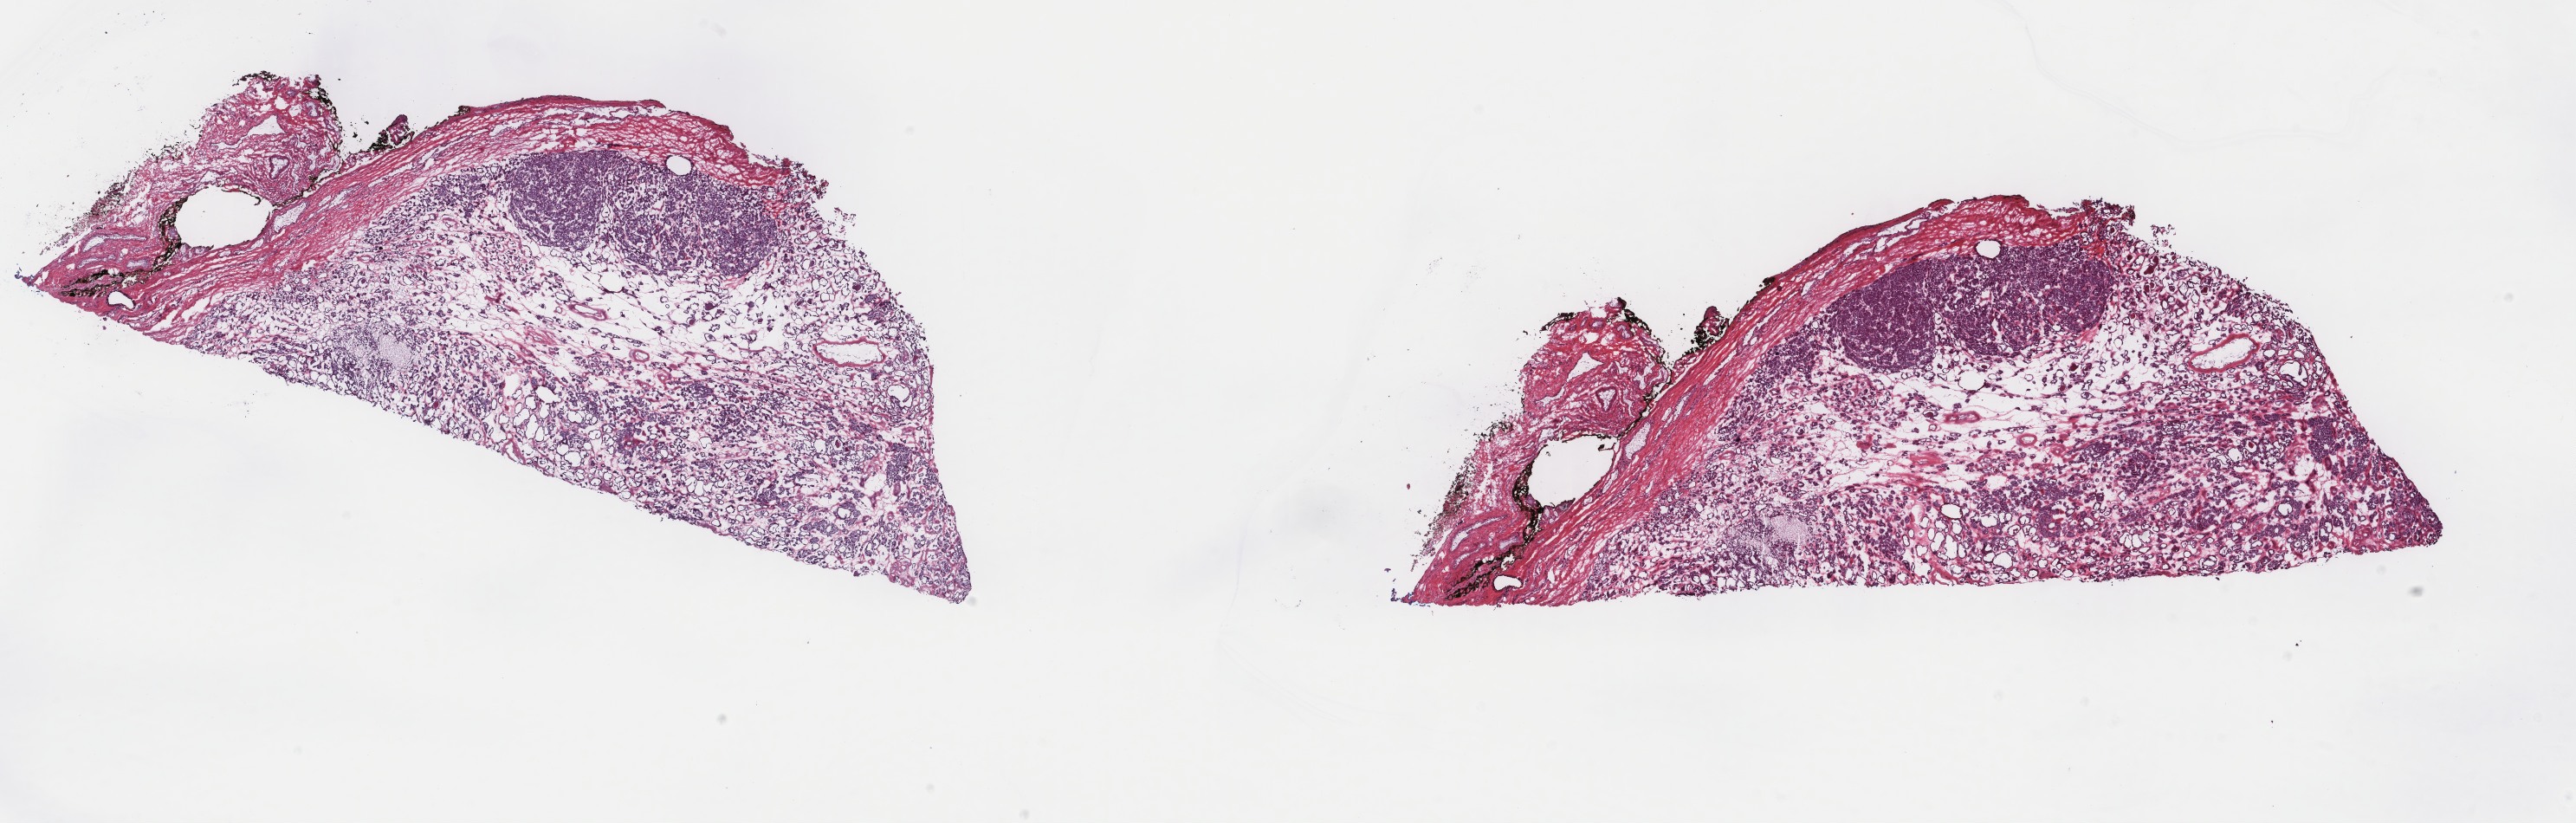
Whole-slide histology image, H&E, whole scanned area (about 23.6 x 7.5 mm) shown as a low-resolution overview, frozen section from the top of the tissue portion, primary tumour sample from the thyroid. Female, age 64 years at initial diagnosis. Composition of this section per pathologist review: tumour cells 75%, tumour nuclei 75%, normal cells 0%, stromal cells 25%, necrosis 0%. Infiltration values recorded for this section: lymphocyte infiltration 3%, monocyte infiltration 0%, neutrophil infiltration 0%.
- pathologic diagnosis: Papillary carcinoma, follicular variant (thyroid gland)
- TNM: T3 N0 MX
- lymph nodes positive (case pathology): 0 of 14 examined
- AJCC pathologic stage: III